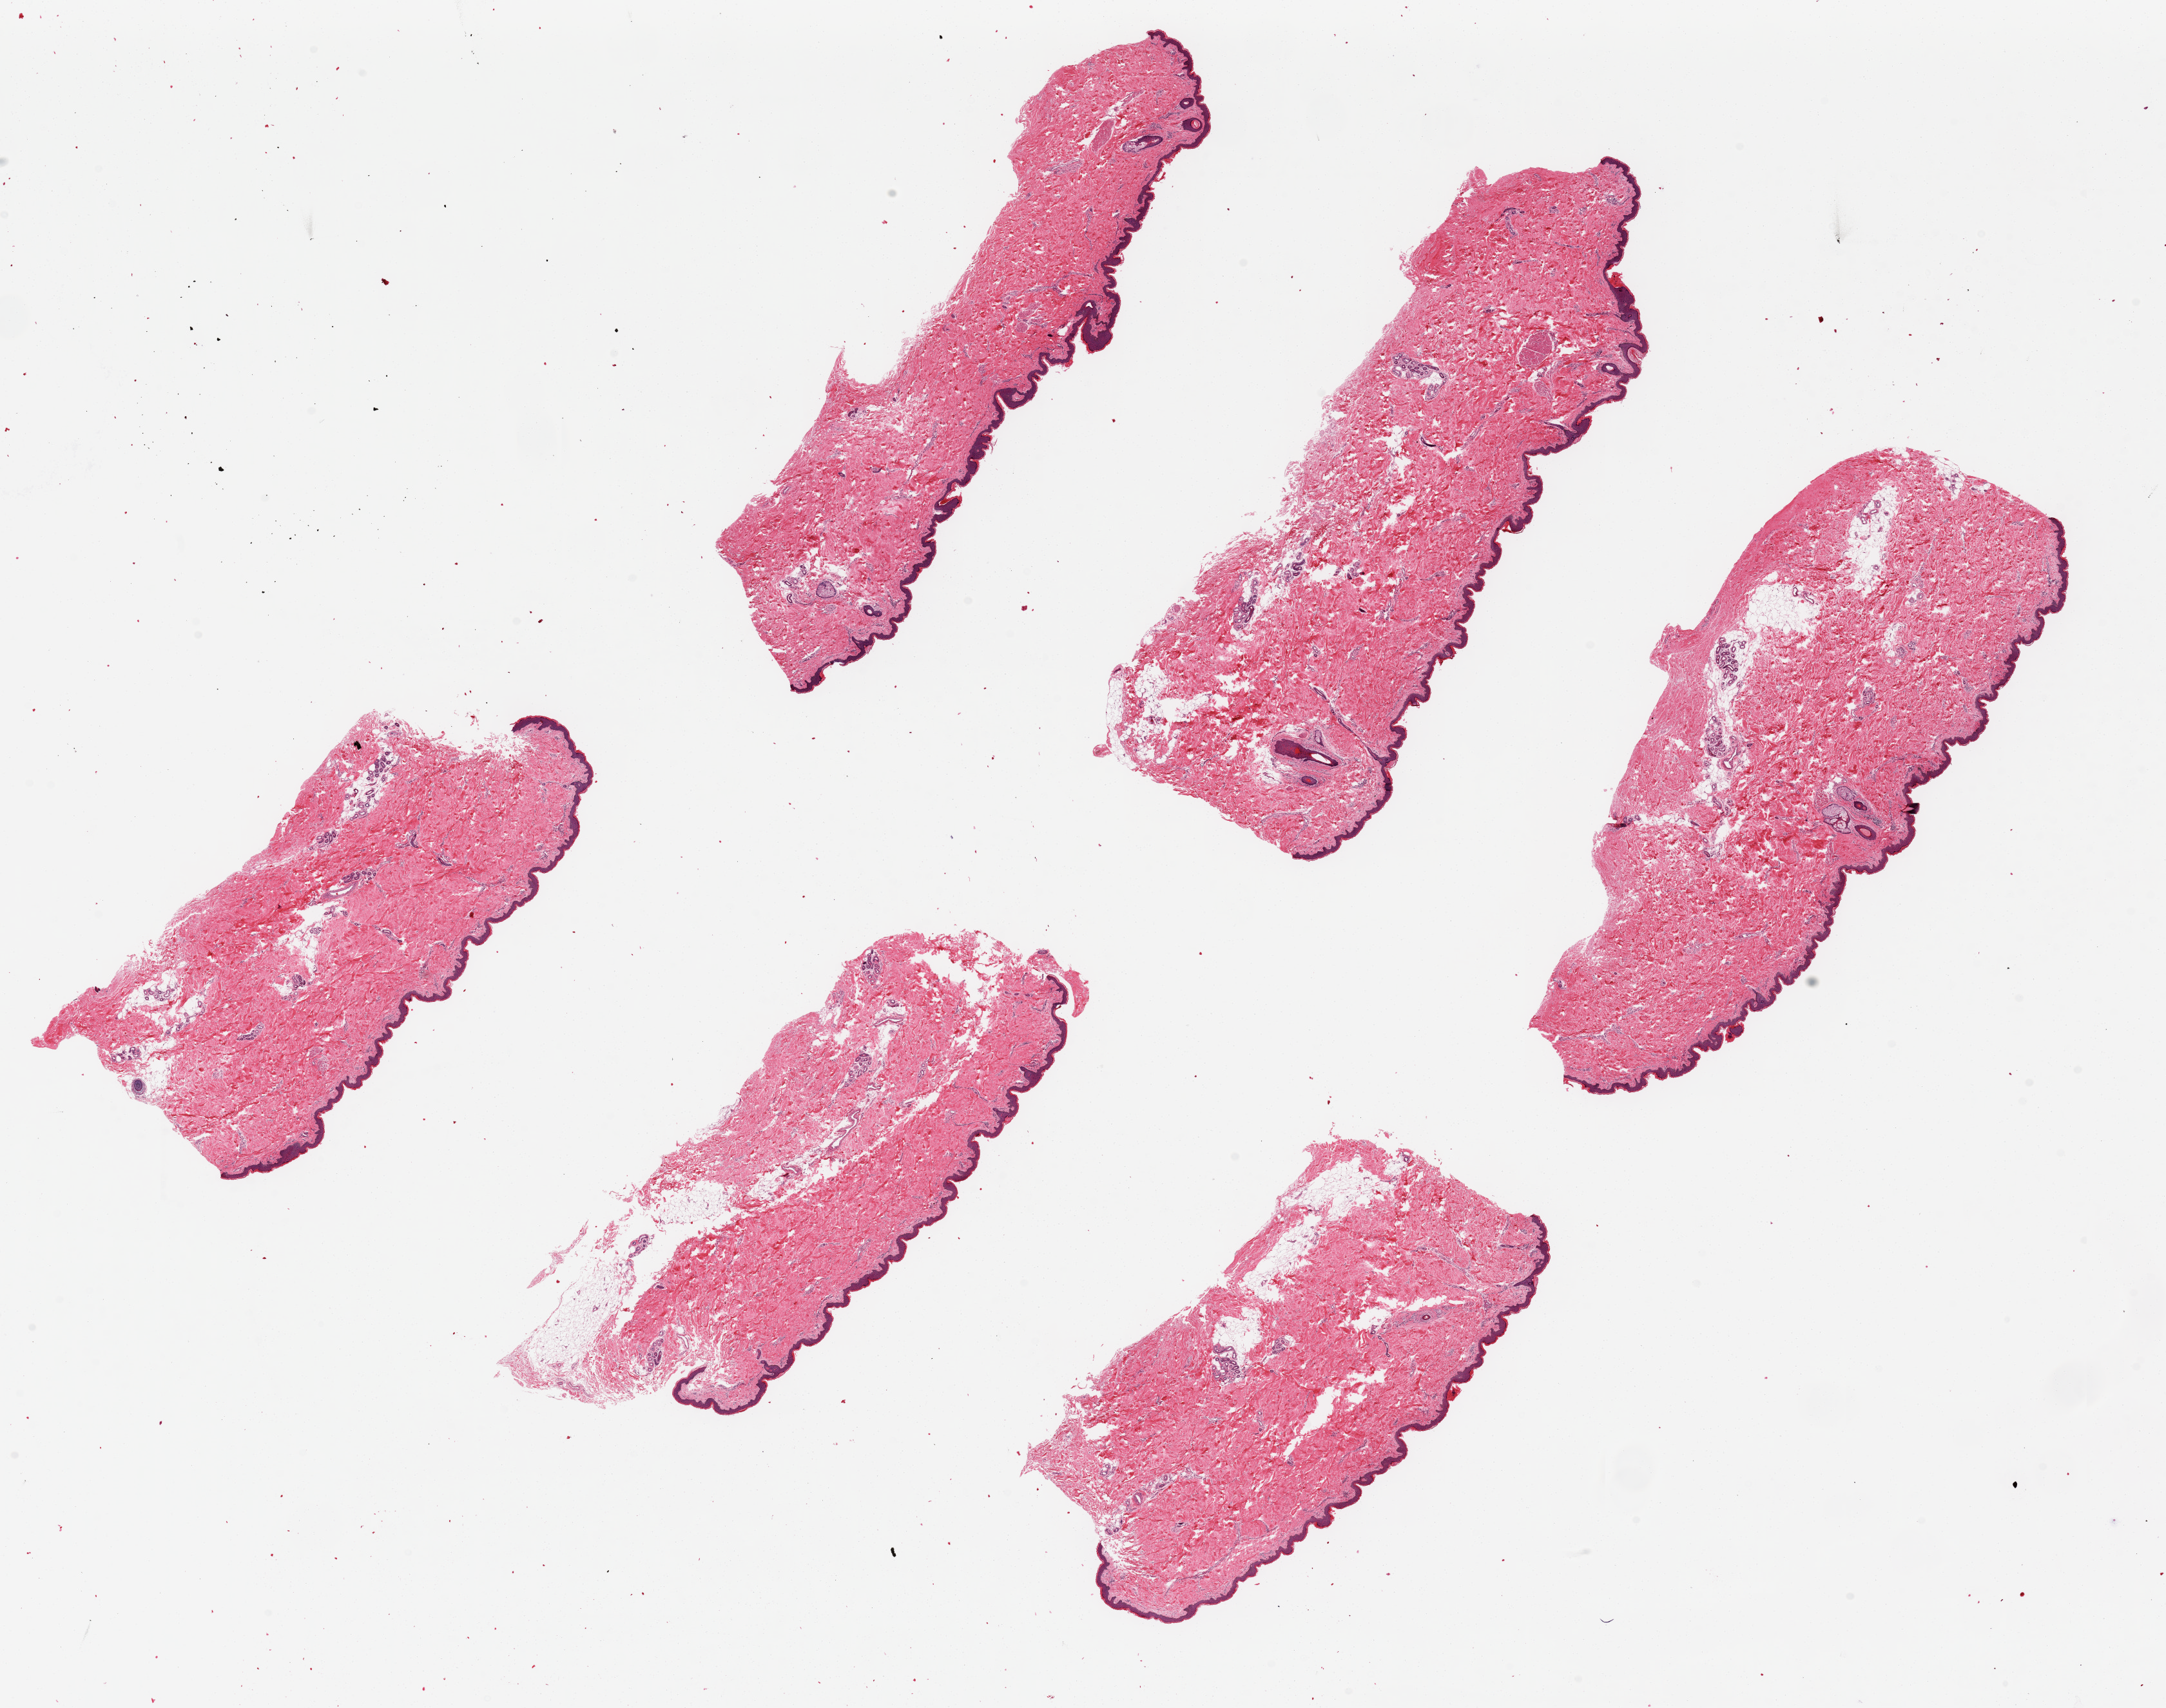
Whole-slide image, haematoxylin and eosin stain, brightfield — whole scanned area (about 26.6 x 21.0 mm) shown as a low-resolution overview. PAXgene-fixed, paraffin-embedded tissue. Section of skin of lower leg (target tissue). Tissue donor sample. Donor: male.
• review note (as recorded): 6 pieces up to 9x3 mm; epidermis 66um thick